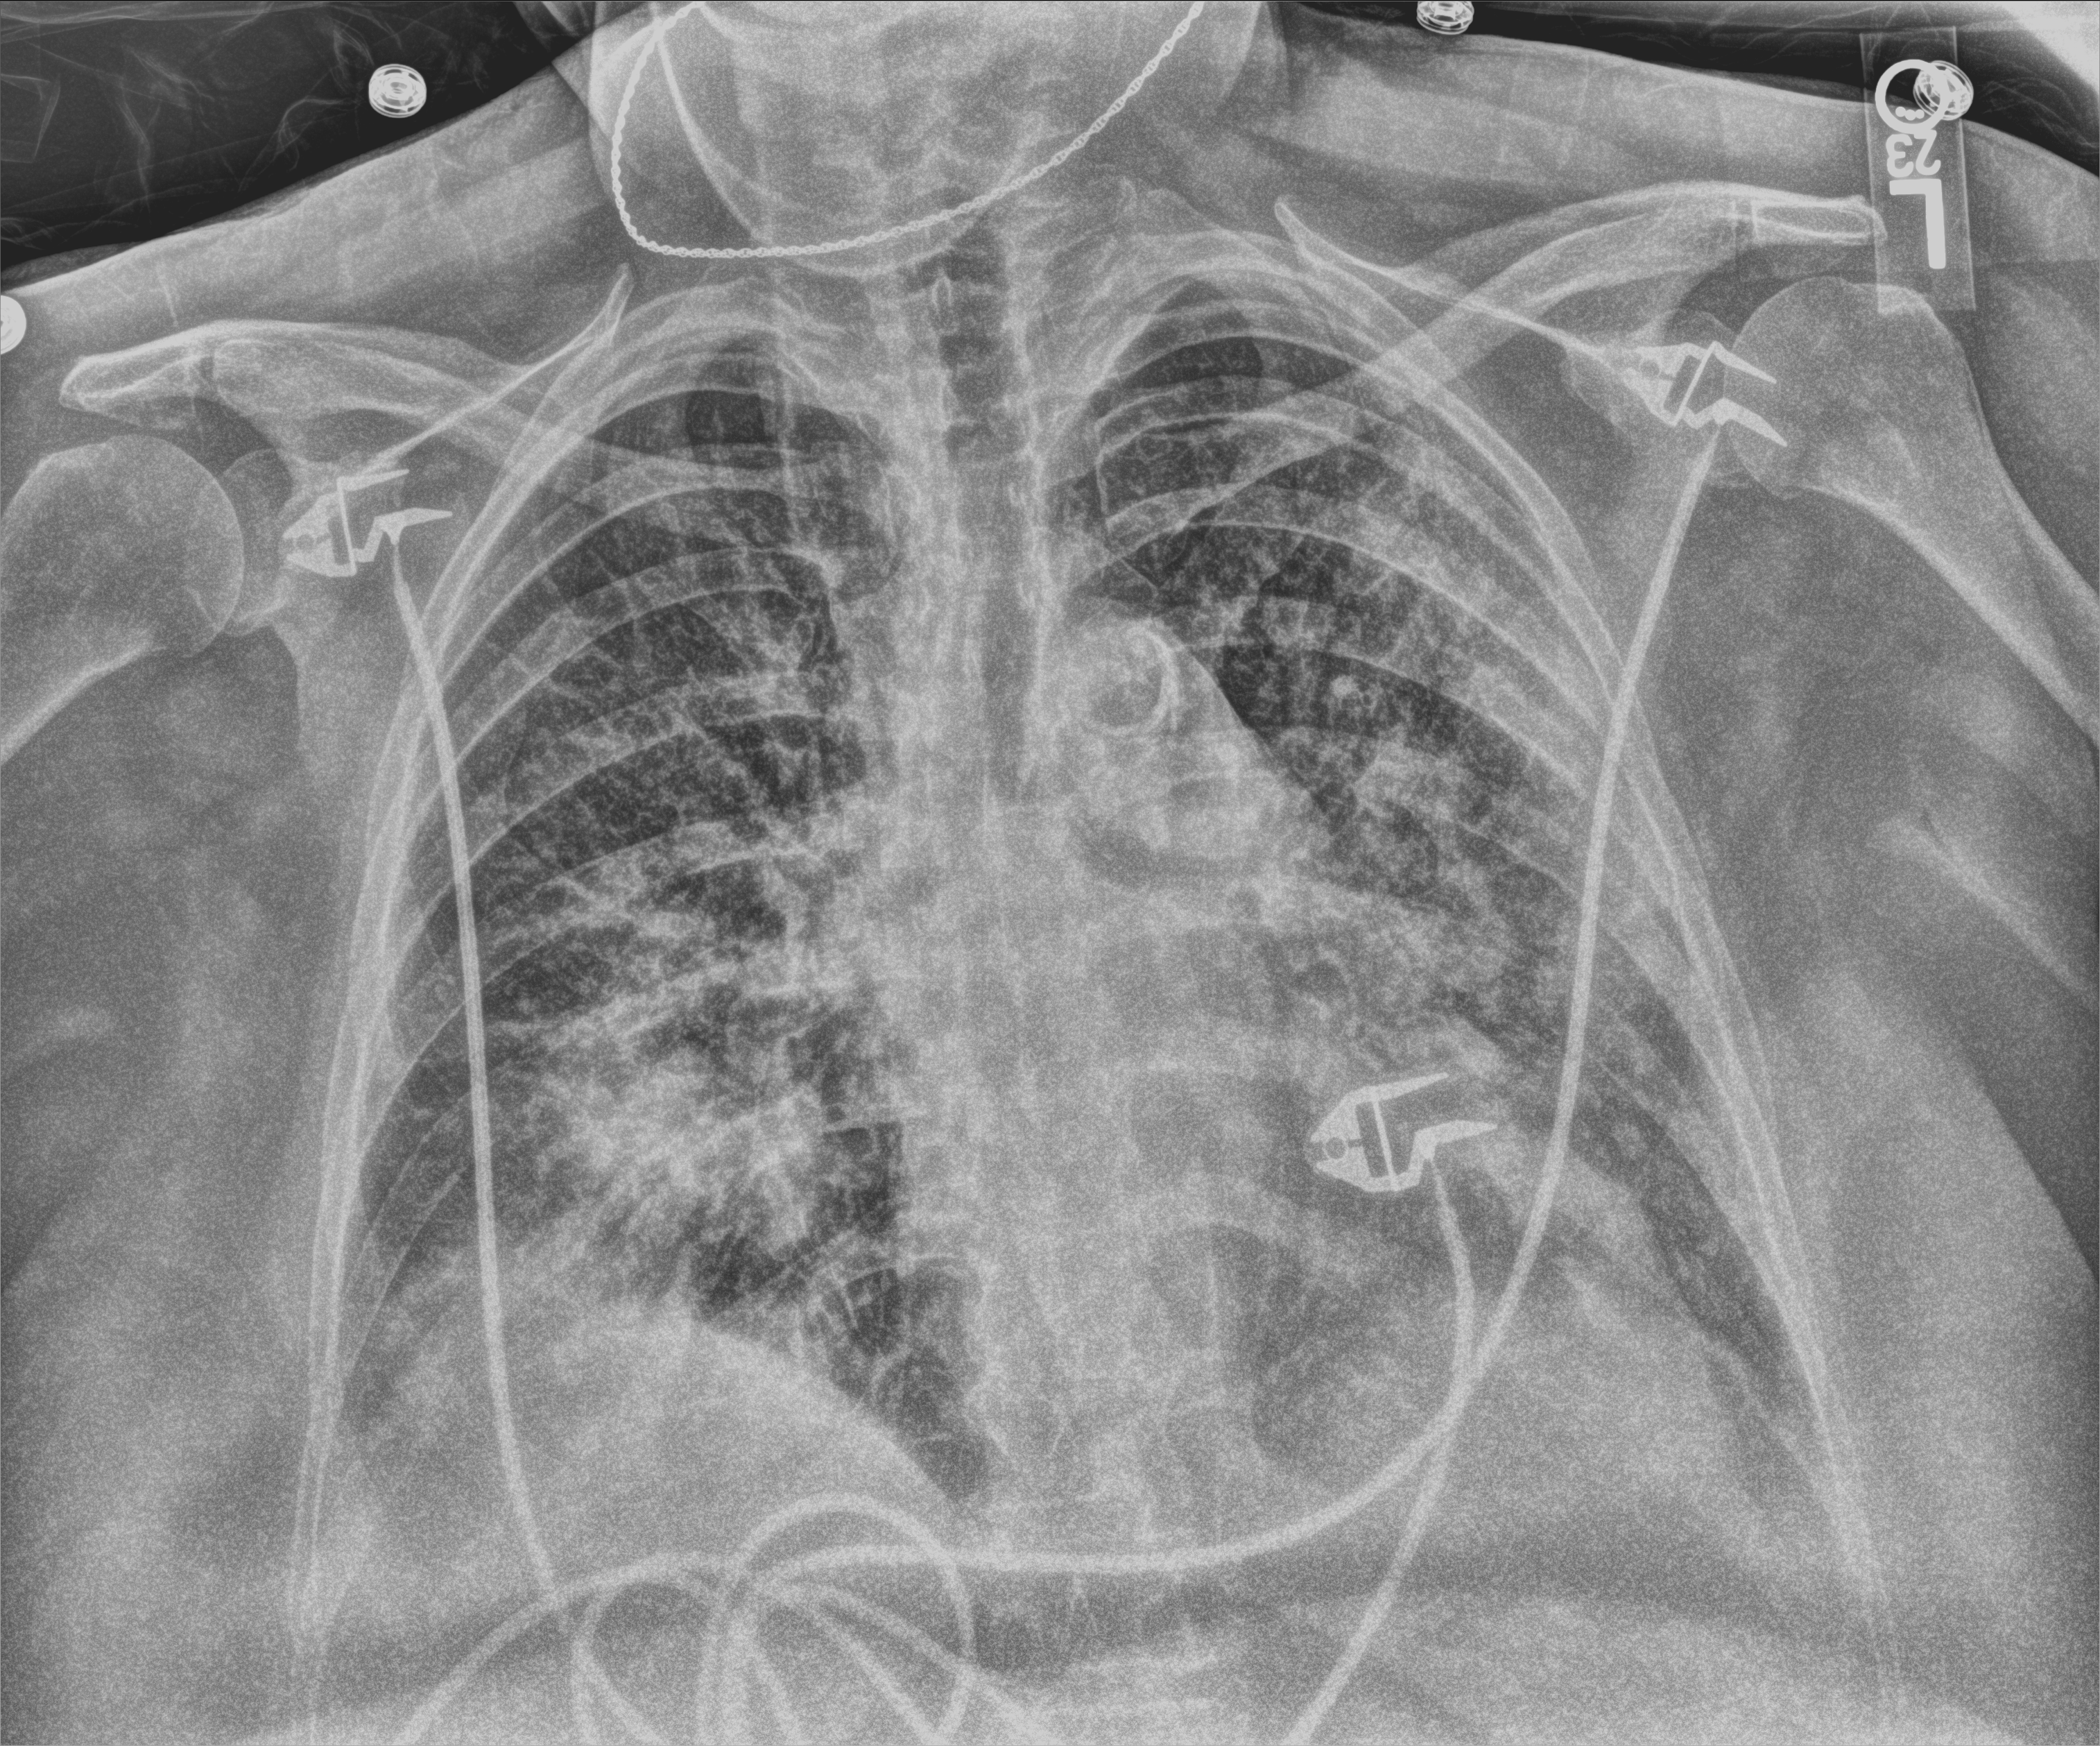
Chest X-ray (portable), anteroposterior (AP) projection. Patient hospitalised with COVID-19; female, aged 60–74 years.
From the hospital-stay record, not from the radiograph (when in the stay this image was taken is not recorded): mechanically ventilated during this hospital stay: no; admitted to intensive care during this hospital stay: no.